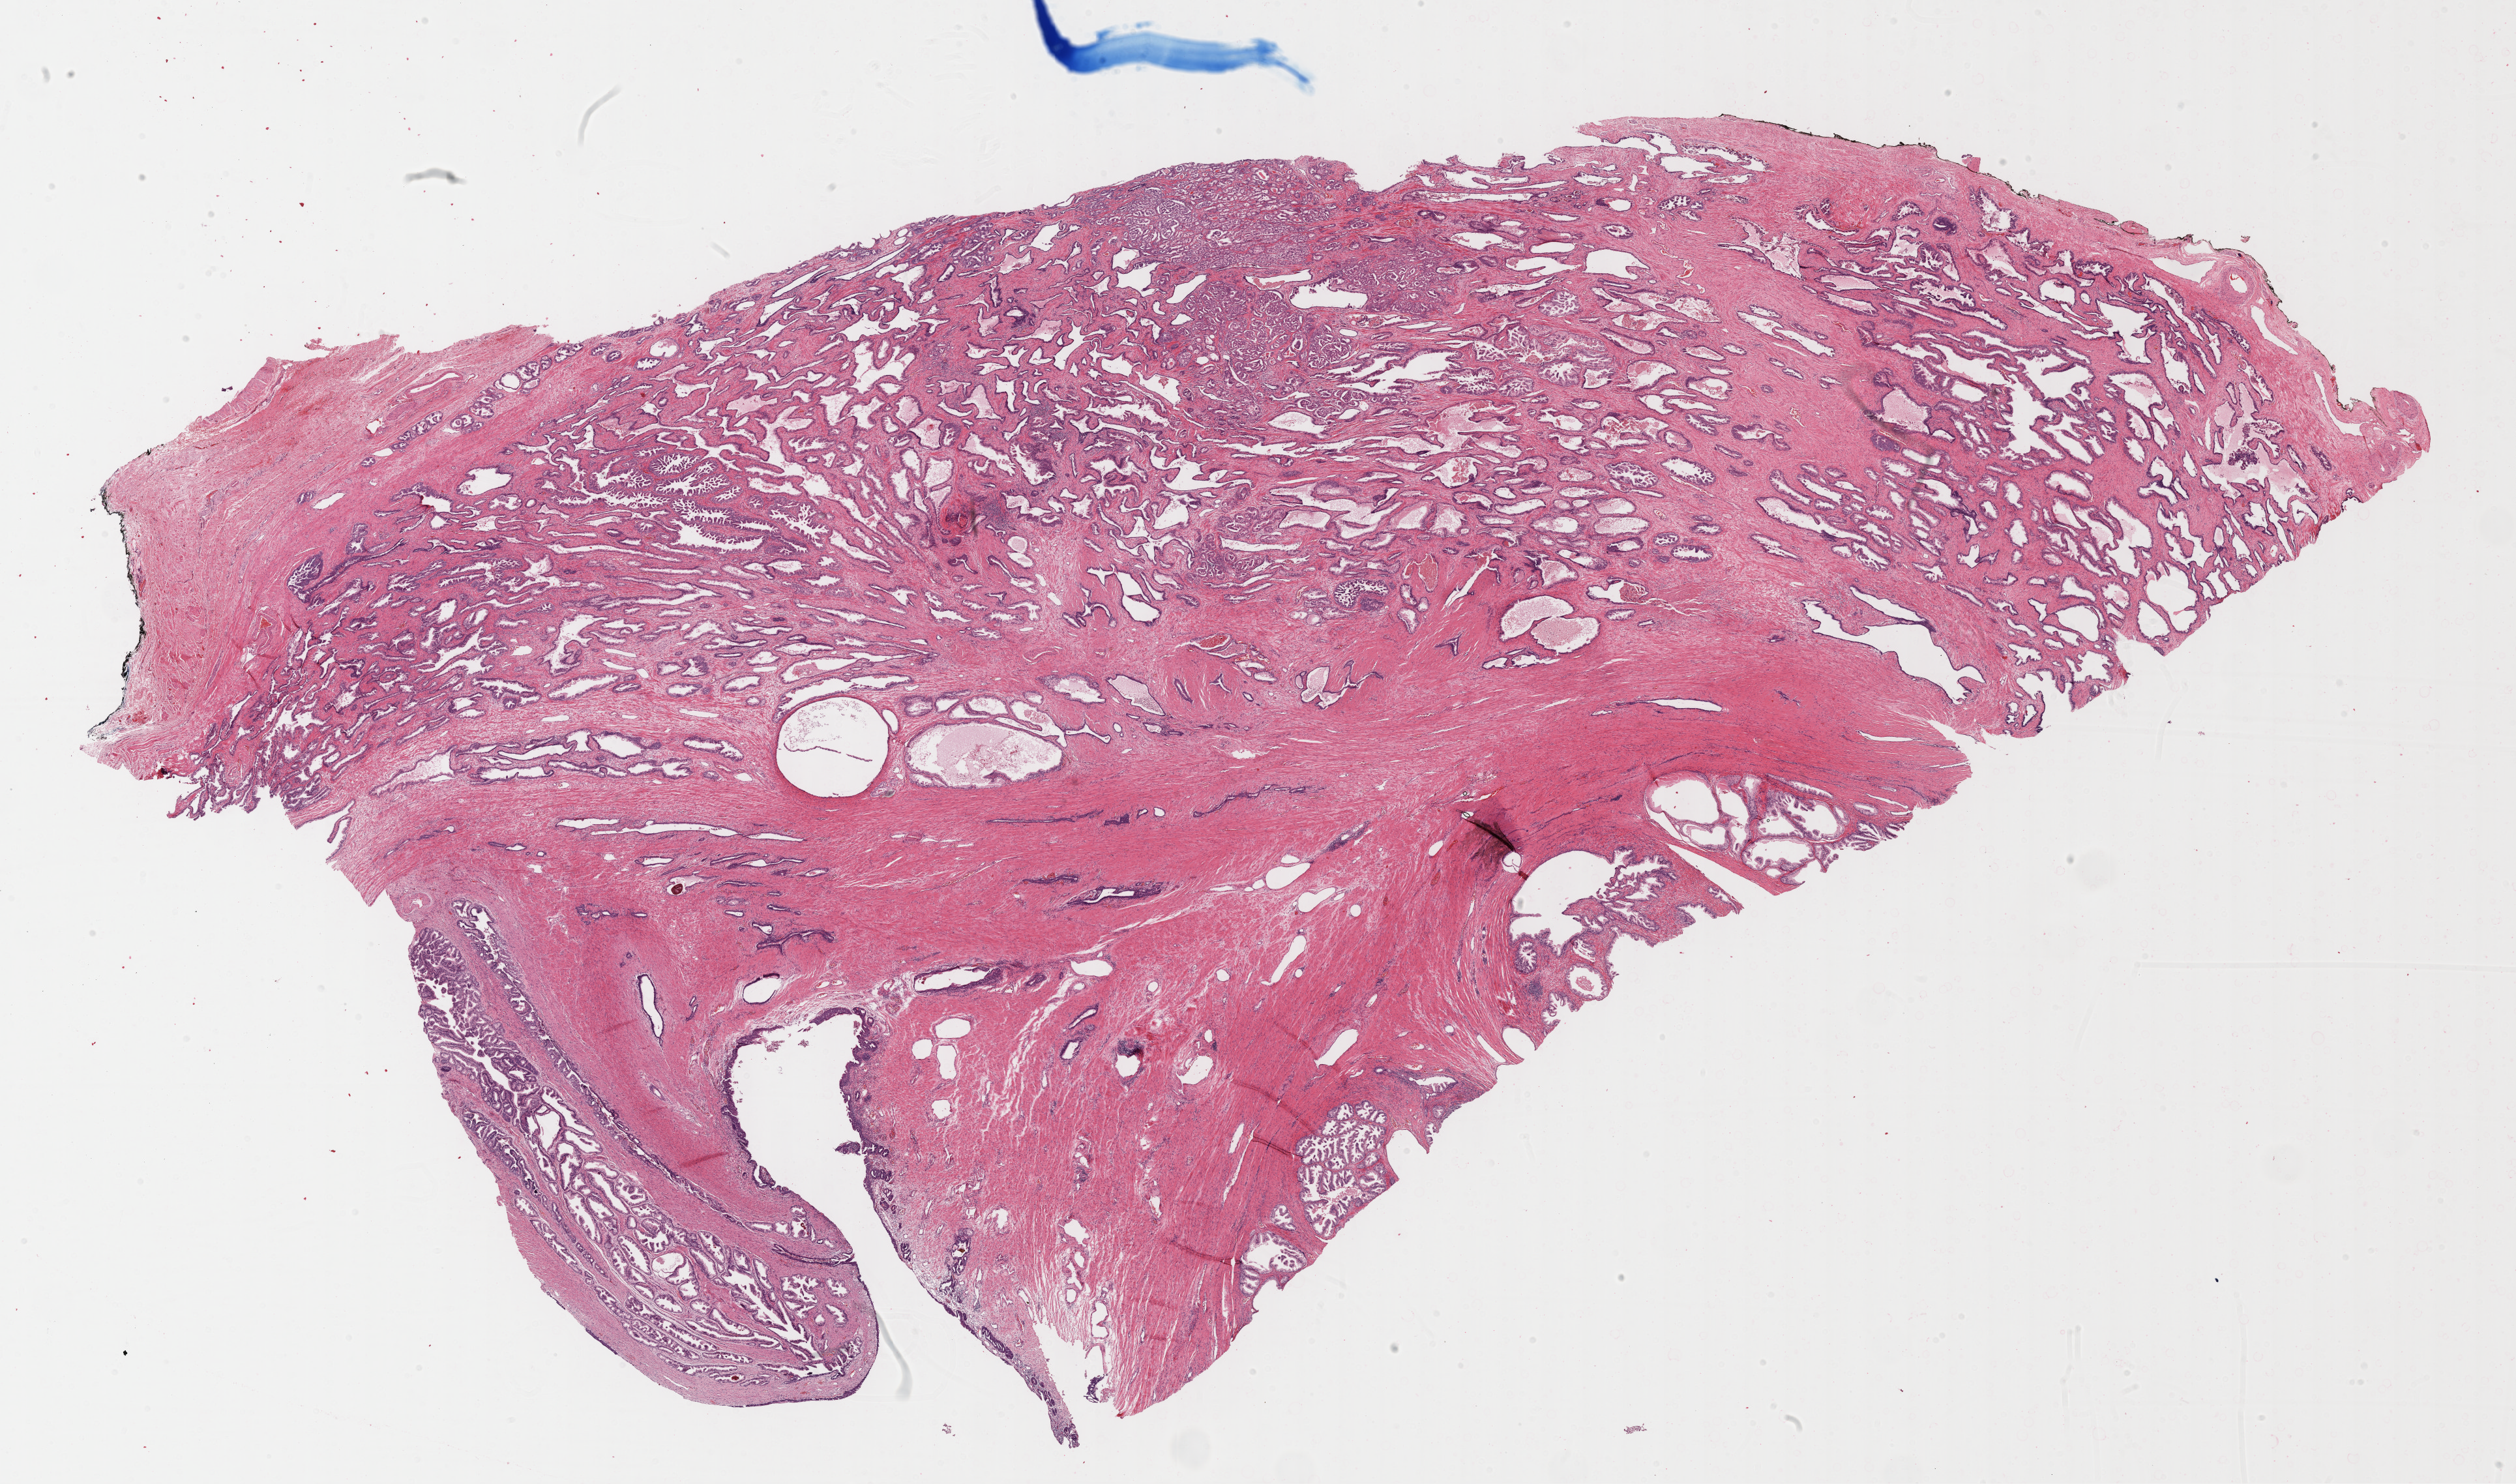
Digitized H&E tissue section (whole slide) — shown as a low-resolution overview of the whole scanned area (about 31.2 x 18.4 mm, acquisition: 40x scan), FFPE section, sample: primary tumour, prostate. Male, age 61 years at initial diagnosis. Gleason score: 7 (3+4).
Pathologic diagnosis: Adenocarcinoma, NOS (prostate gland). Lymph nodes positive (case pathology): 0 of 5 examined.